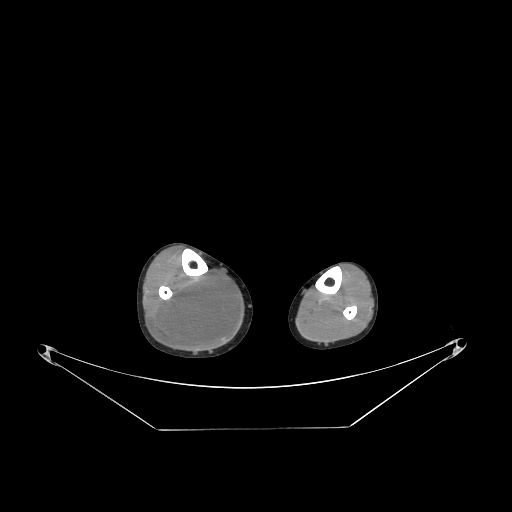
CT of an extremity soft-tissue mass (from a PET/CT study), one axial slice. Slice 91 of 267 in the series (ordered by position). Reconstruction kernel STANDARD. 140 kVp. Soft-tissue window (W 400 / L 40 HU). 3.75 mm slice thickness. 512 × 512 image matrix. Male patient. Case-level facts recorded for this patient, not image findings: histological type: liposarcoma - round cell; grade: high; site of the primary tumour: right calf.
Outlined on this slice (expert contour drawn on MRI and transferred to this co-registered scan by the dataset authors):
- gross tumour volume (mass): bounding box <153,274,239,348> (left, top, right, bottom; pixels)